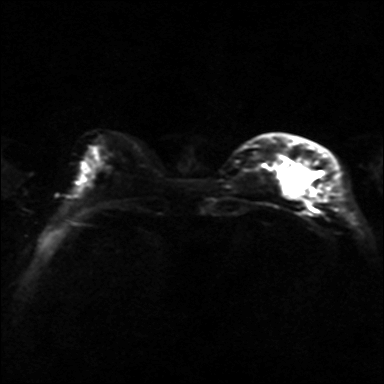
Breast MRI, one axial slice; position 10 of 36 along the scan axis; diffusion-weighted series; image 2 of 4 stored at this slice position (different b-values; order by instance number); 3 T; 4 mm slice thickness; 384 × 384 image matrix. Female patient.
Structures marked on this image (outlined manually by an expert reader):
- tumour on diffusion-weighted imaging: bounding box [x1, y1, x2, y2] px = [282, 163, 315, 197]